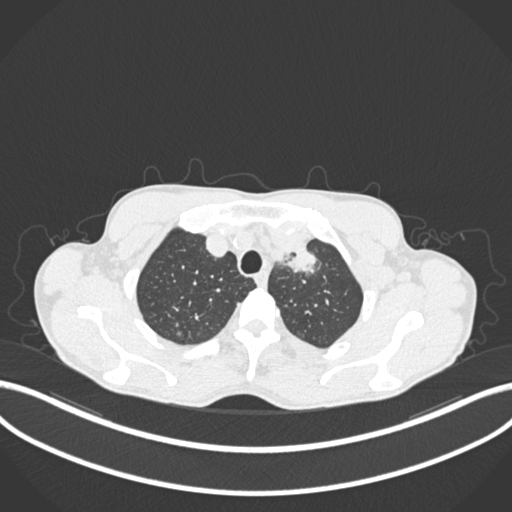
Chest CT, one axial slice. Slice 175 of 211 in the series (ordered by position). 120 kVp. Lung window (W 1500 / L -600 HU). 512 × 512 image matrix, field of view 400 × 400 mm. Male patient, age 58 years. From the clinical record (not read from this slice): clinical TNM (as recorded): T1c N1 M0.
Outlined on this slice (bounding box drawn by a radiologist):
- lung tumour (recorded histology: adenocarcinoma): bounding box <279,242,323,282> (left, top, right, bottom; pixels)